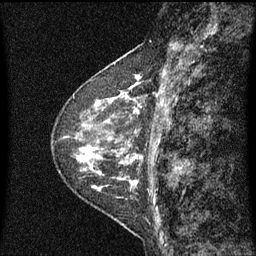
Breast MRI (dynamic contrast-enhanced), one sagittal slice. Slice 25 of 60 in the series (ordered by position). Dynamic contrast-enhanced series, image 2 of 3 at this slice position (ordered by acquisition). 1.5 T. TE 4.2 ms, TR 8 ms. 2 mm slice thickness. 256 × 256 image matrix, field of view 200 × 200 mm. Patient: female, 48 years.
Structures marked on this image (semi-automatically segmented with operator editing):
- analysis volume of interest (the breast-tissue region the enhancement analysis was run in; not a lesion): bounding box [x1, y1, x2, y2] px = [103, 74, 145, 139]
- tumour enhancement mask (voxels above the 70 % enhancement threshold inside the analysis volume of interest): [116, 74, 142, 115]